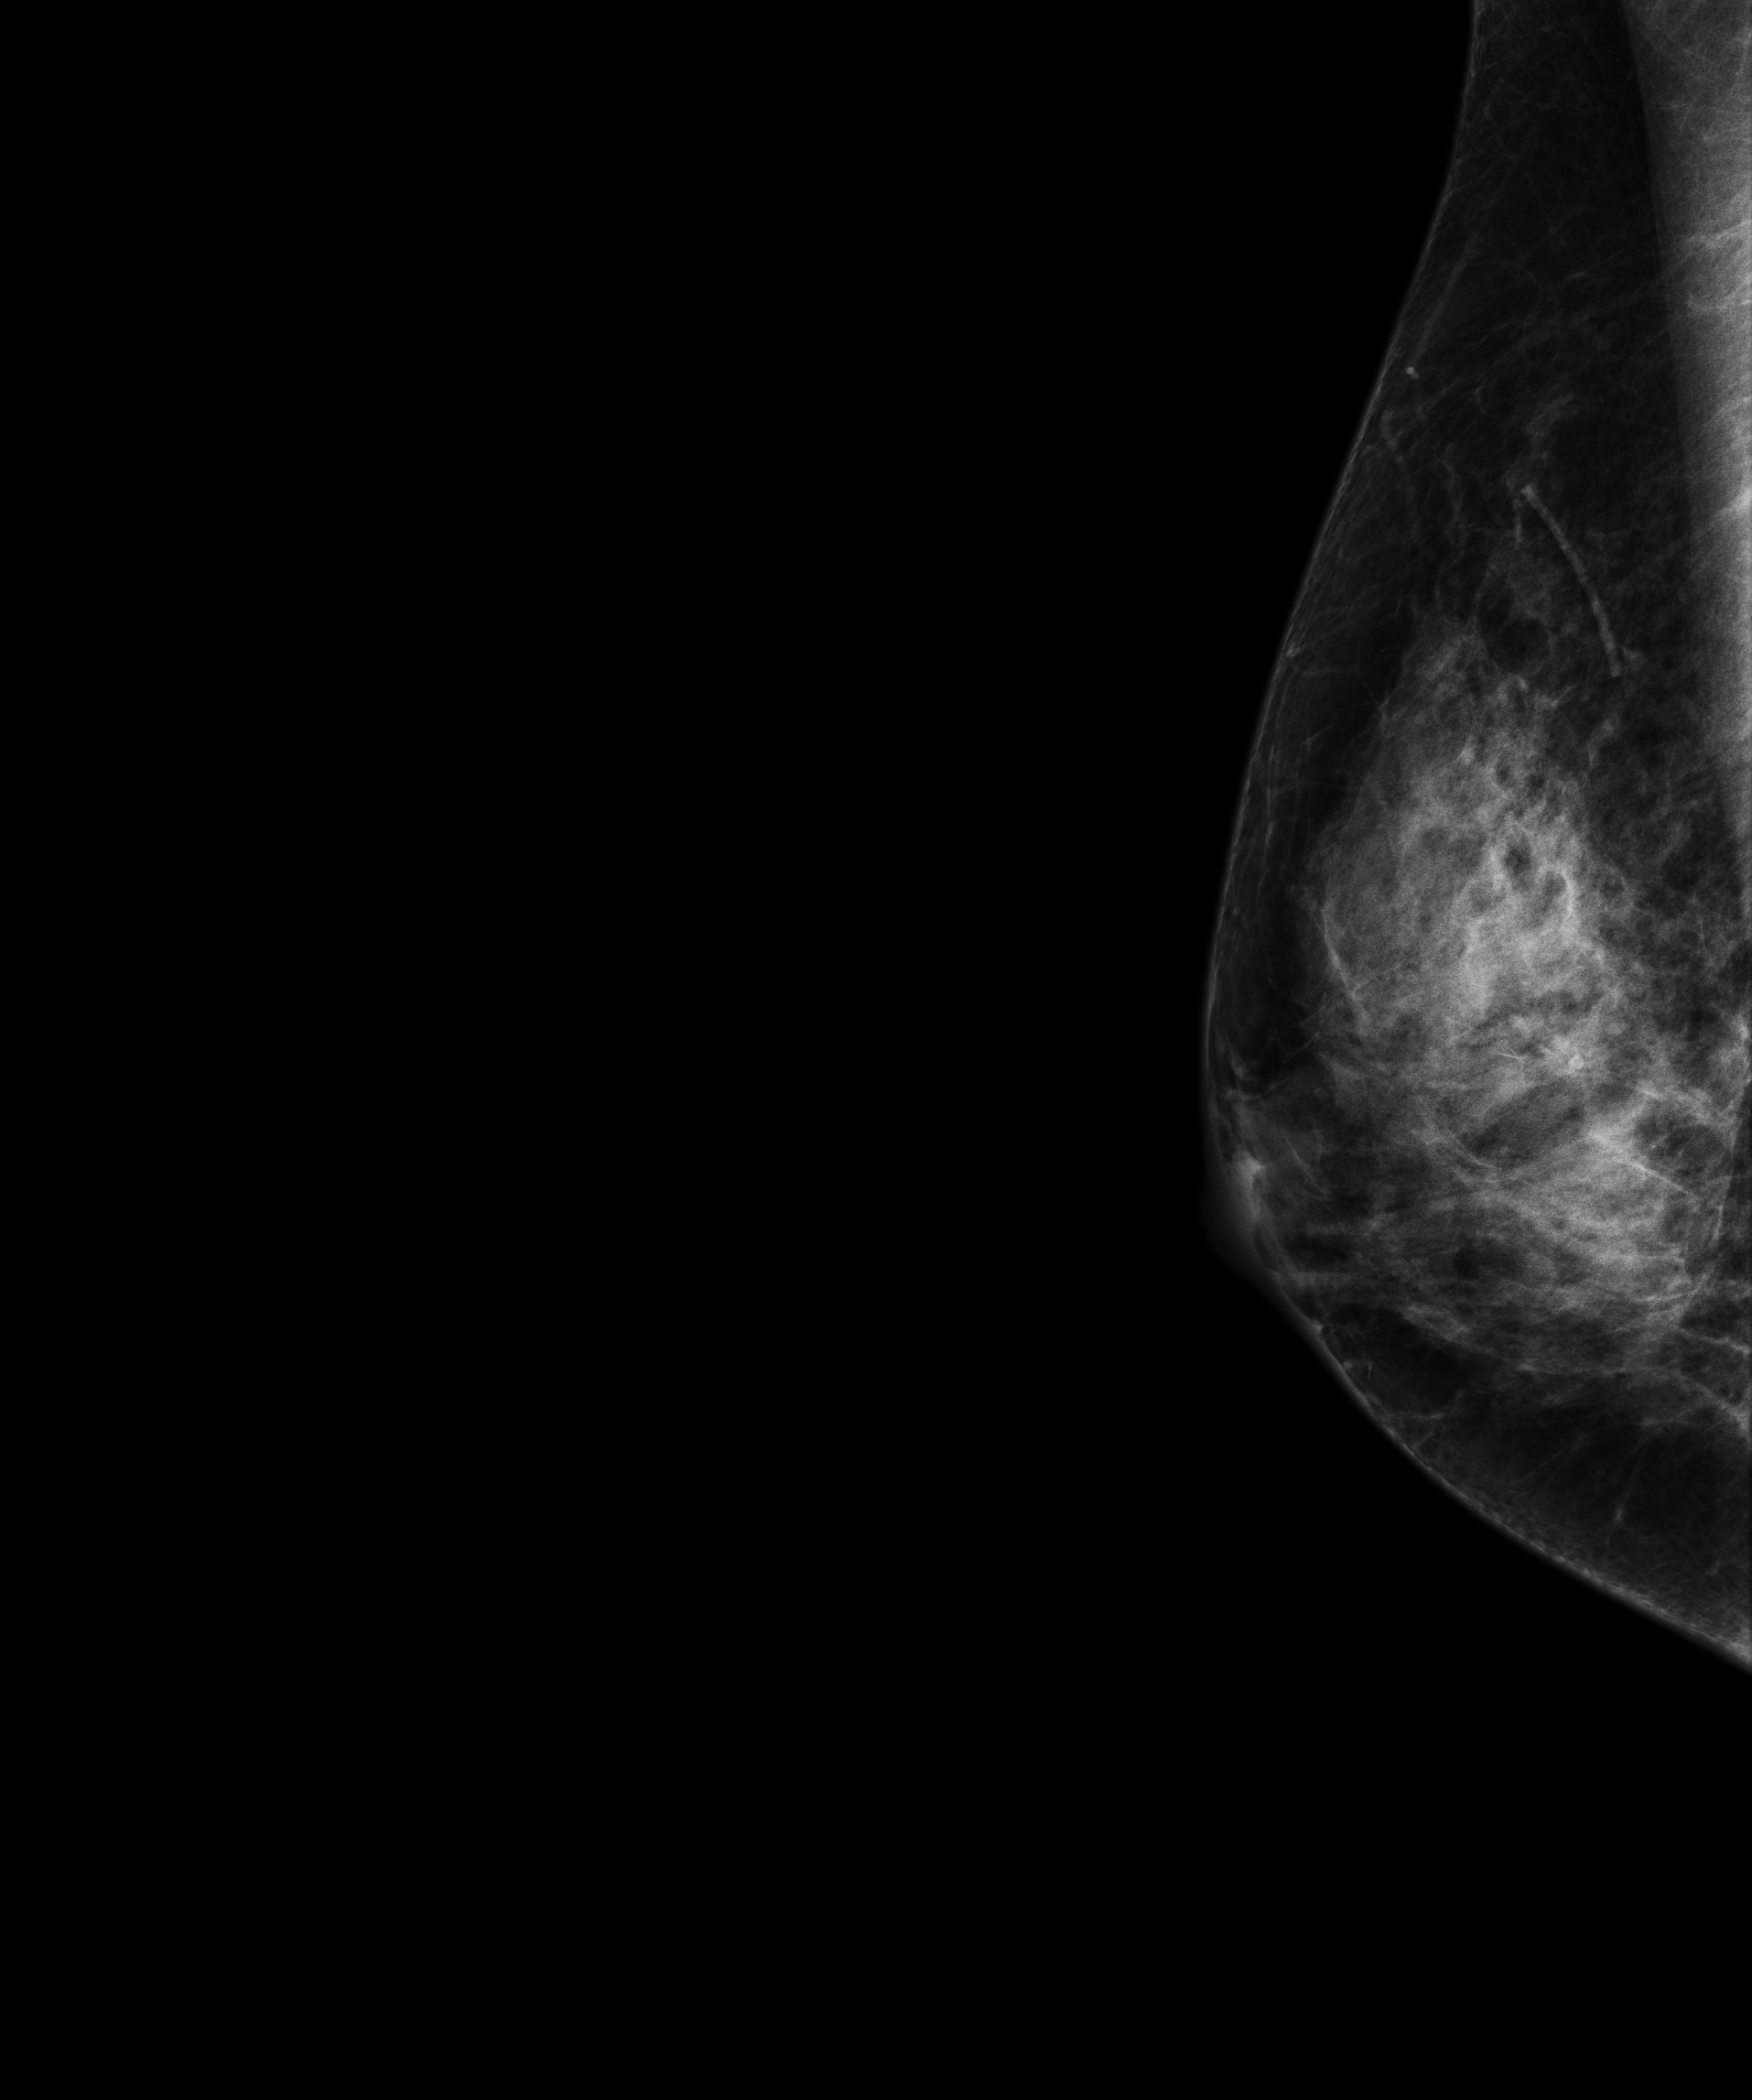
Annual screening mammography examination; compressed breast thickness 58 mm. Female patient, age 55 years.
Image type: full-field digital mammogram. Breast: right. Projection: laterally exaggerated craniocaudal (XCCL) view.